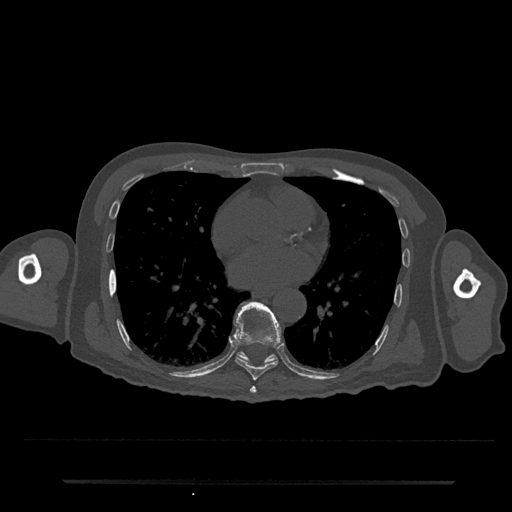
CT including the spine, one axial slice; reconstruction kernel Br40s/3; 120 kVp; bone window (W 1800 / L 400 HU); 0.5 mm slice thickness; 512 × 512 image matrix. Patient: male, 74 years. Case-level facts recorded for this patient, not image findings: primary cancer: prostate.
Outlined on this slice (semi-automatic segmentation, software-assisted and operator-edited):
- T7 vertebra: bounding box (x1, y1, x2, y2) in pixels: (250, 386, 256, 394)
- T8 vertebra: (234, 301, 282, 380)
- T9 vertebra: (238, 352, 277, 362)